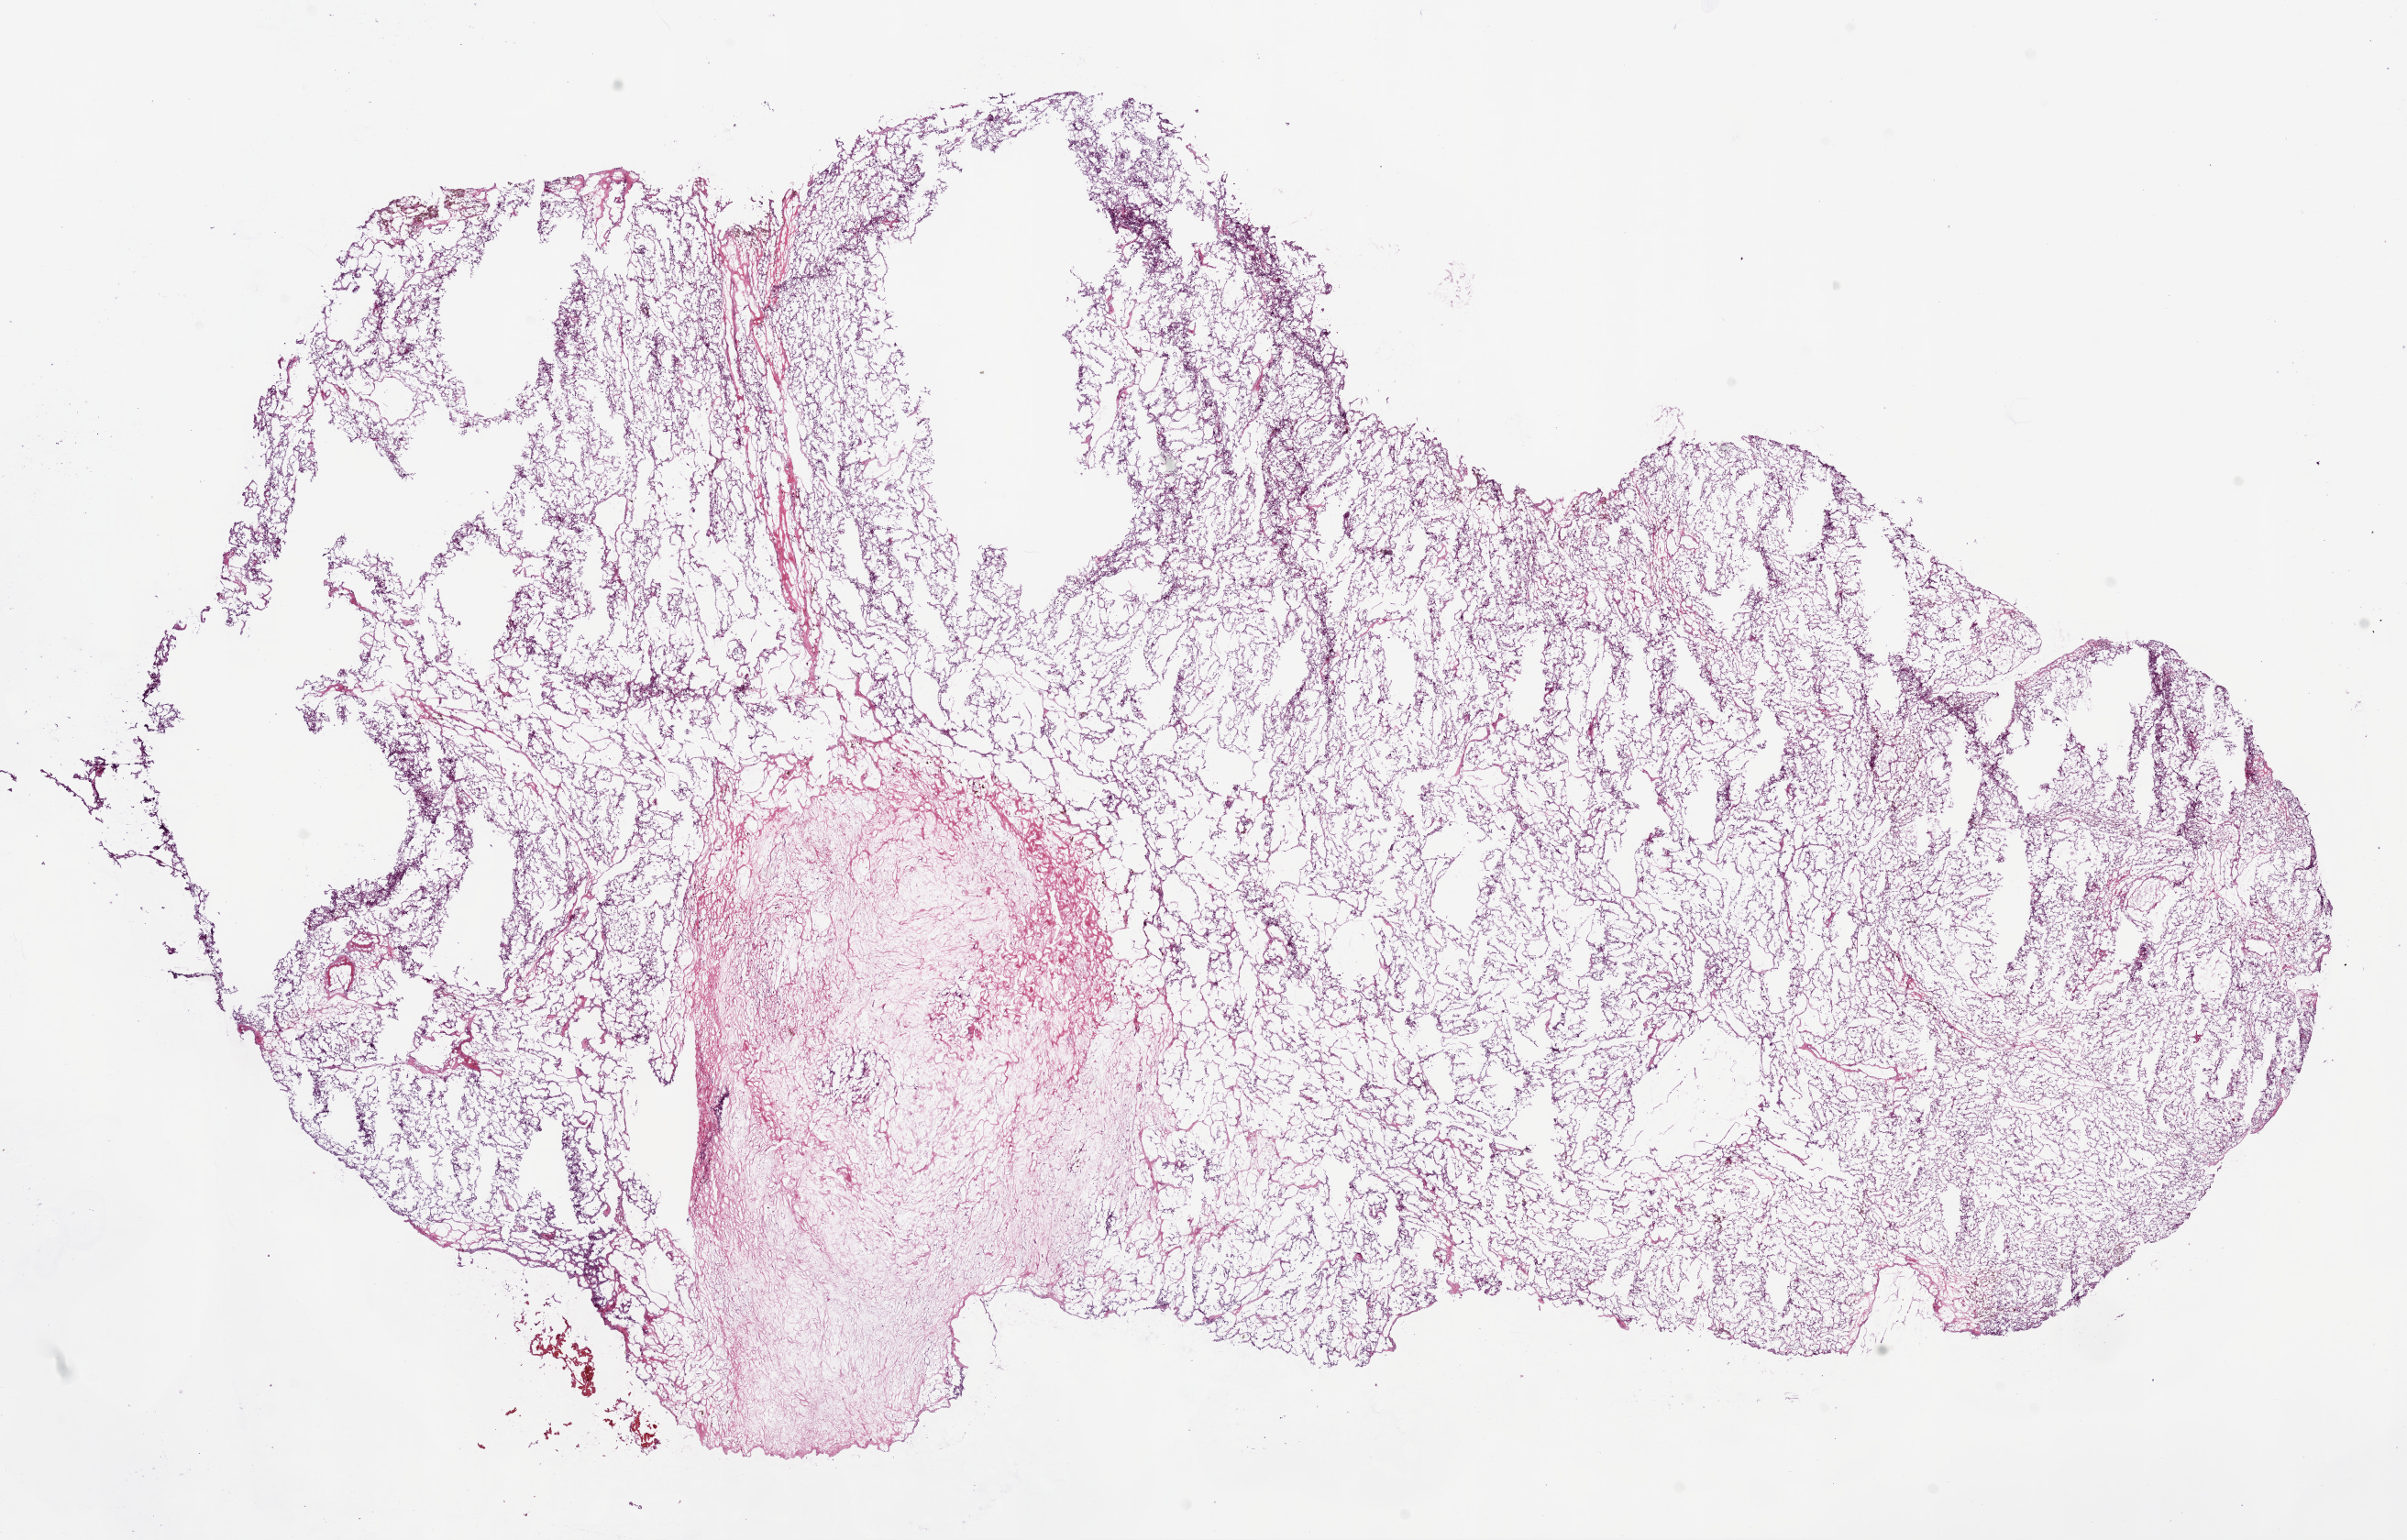
H&E whole-slide image — whole scanned area (about 21.1 x 13.5 mm) shown as a low-resolution overview; frozen section from the bottom of the tissue portion; kidney, primary tumour sample. Male patient; age at initial diagnosis 55 years. Histologic grade: G2 (moderately differentiated). Slide review estimates, as recorded: tumour cells 80%, tumour nuclei 80%, normal cells 0%, stromal cells 20%, necrosis 0%.
* AJCC pathologic stage: I
* pathologic diagnosis: Clear cell adenocarcinoma, NOS